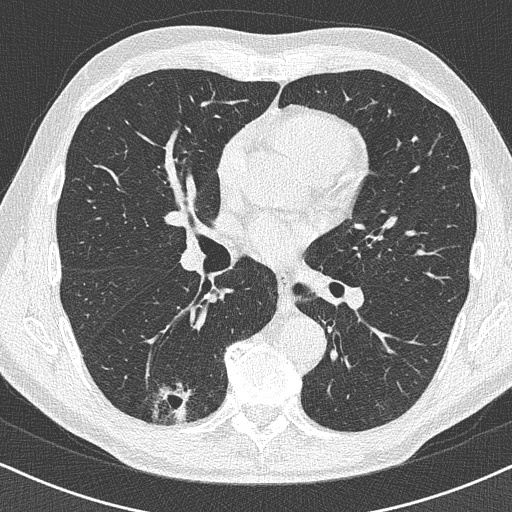
Low-dose screening chest CT, one axial slice; position 229 of 438 along the scan axis; reconstruction kernel B50f; lung window (W 1500 / L -600 HU); 1 mm slice thickness; 512 × 512 image matrix, field of view 320 × 320 mm.
Structures marked on this image (outlined manually by an expert reader):
- lesion 1 (tumor, lower lobe of right lung): bounding box [x1, y1, x2, y2] px = [175, 404, 189, 423]